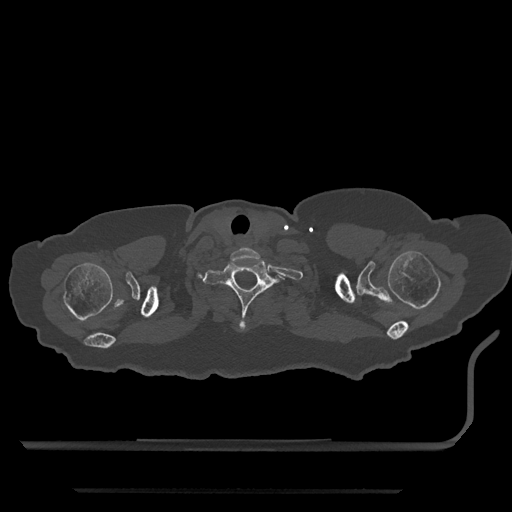
CT including the spine, one axial slice. Slice 713 of 797 in the series (ordered by position). Reconstruction kernel Br40s/3. 120 kVp. Bone window (W 1800 / L 400 HU). 512 × 512 image matrix. Patient: female, 51 years. Case-level facts recorded for this patient, not image findings: primary cancer: neuro; vertebrae with lytic lesions (as recorded): T8.
Structures marked on this image (semi-automatic segmentation, software-assisted and operator-edited):
- T1 vertebra: bounding box <203,260,285,331> (left, top, right, bottom; pixels)